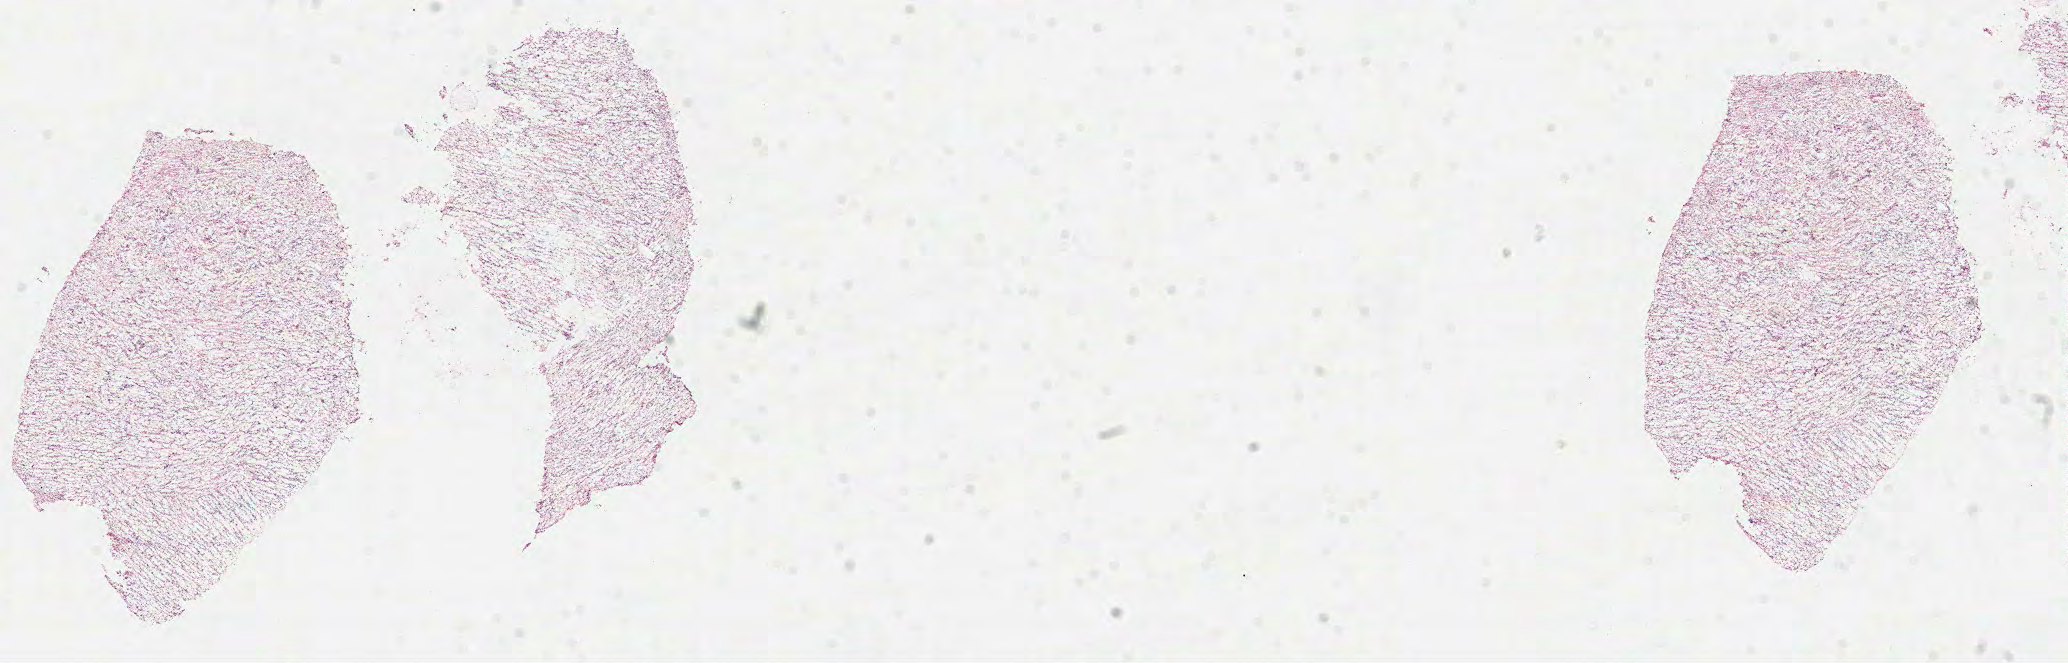
Digitized H&E-stained tissue section (whole slide) — low-resolution overview of the scanned area, about 16.7 x 5.3 mm (from a 40x scan); formalin-fixed paraffin-embedded (FFPE) diagnostic section; primary tumour sample from the brain. Male patient; age at initial diagnosis 48 years.
* pathologic diagnosis: Glioblastoma